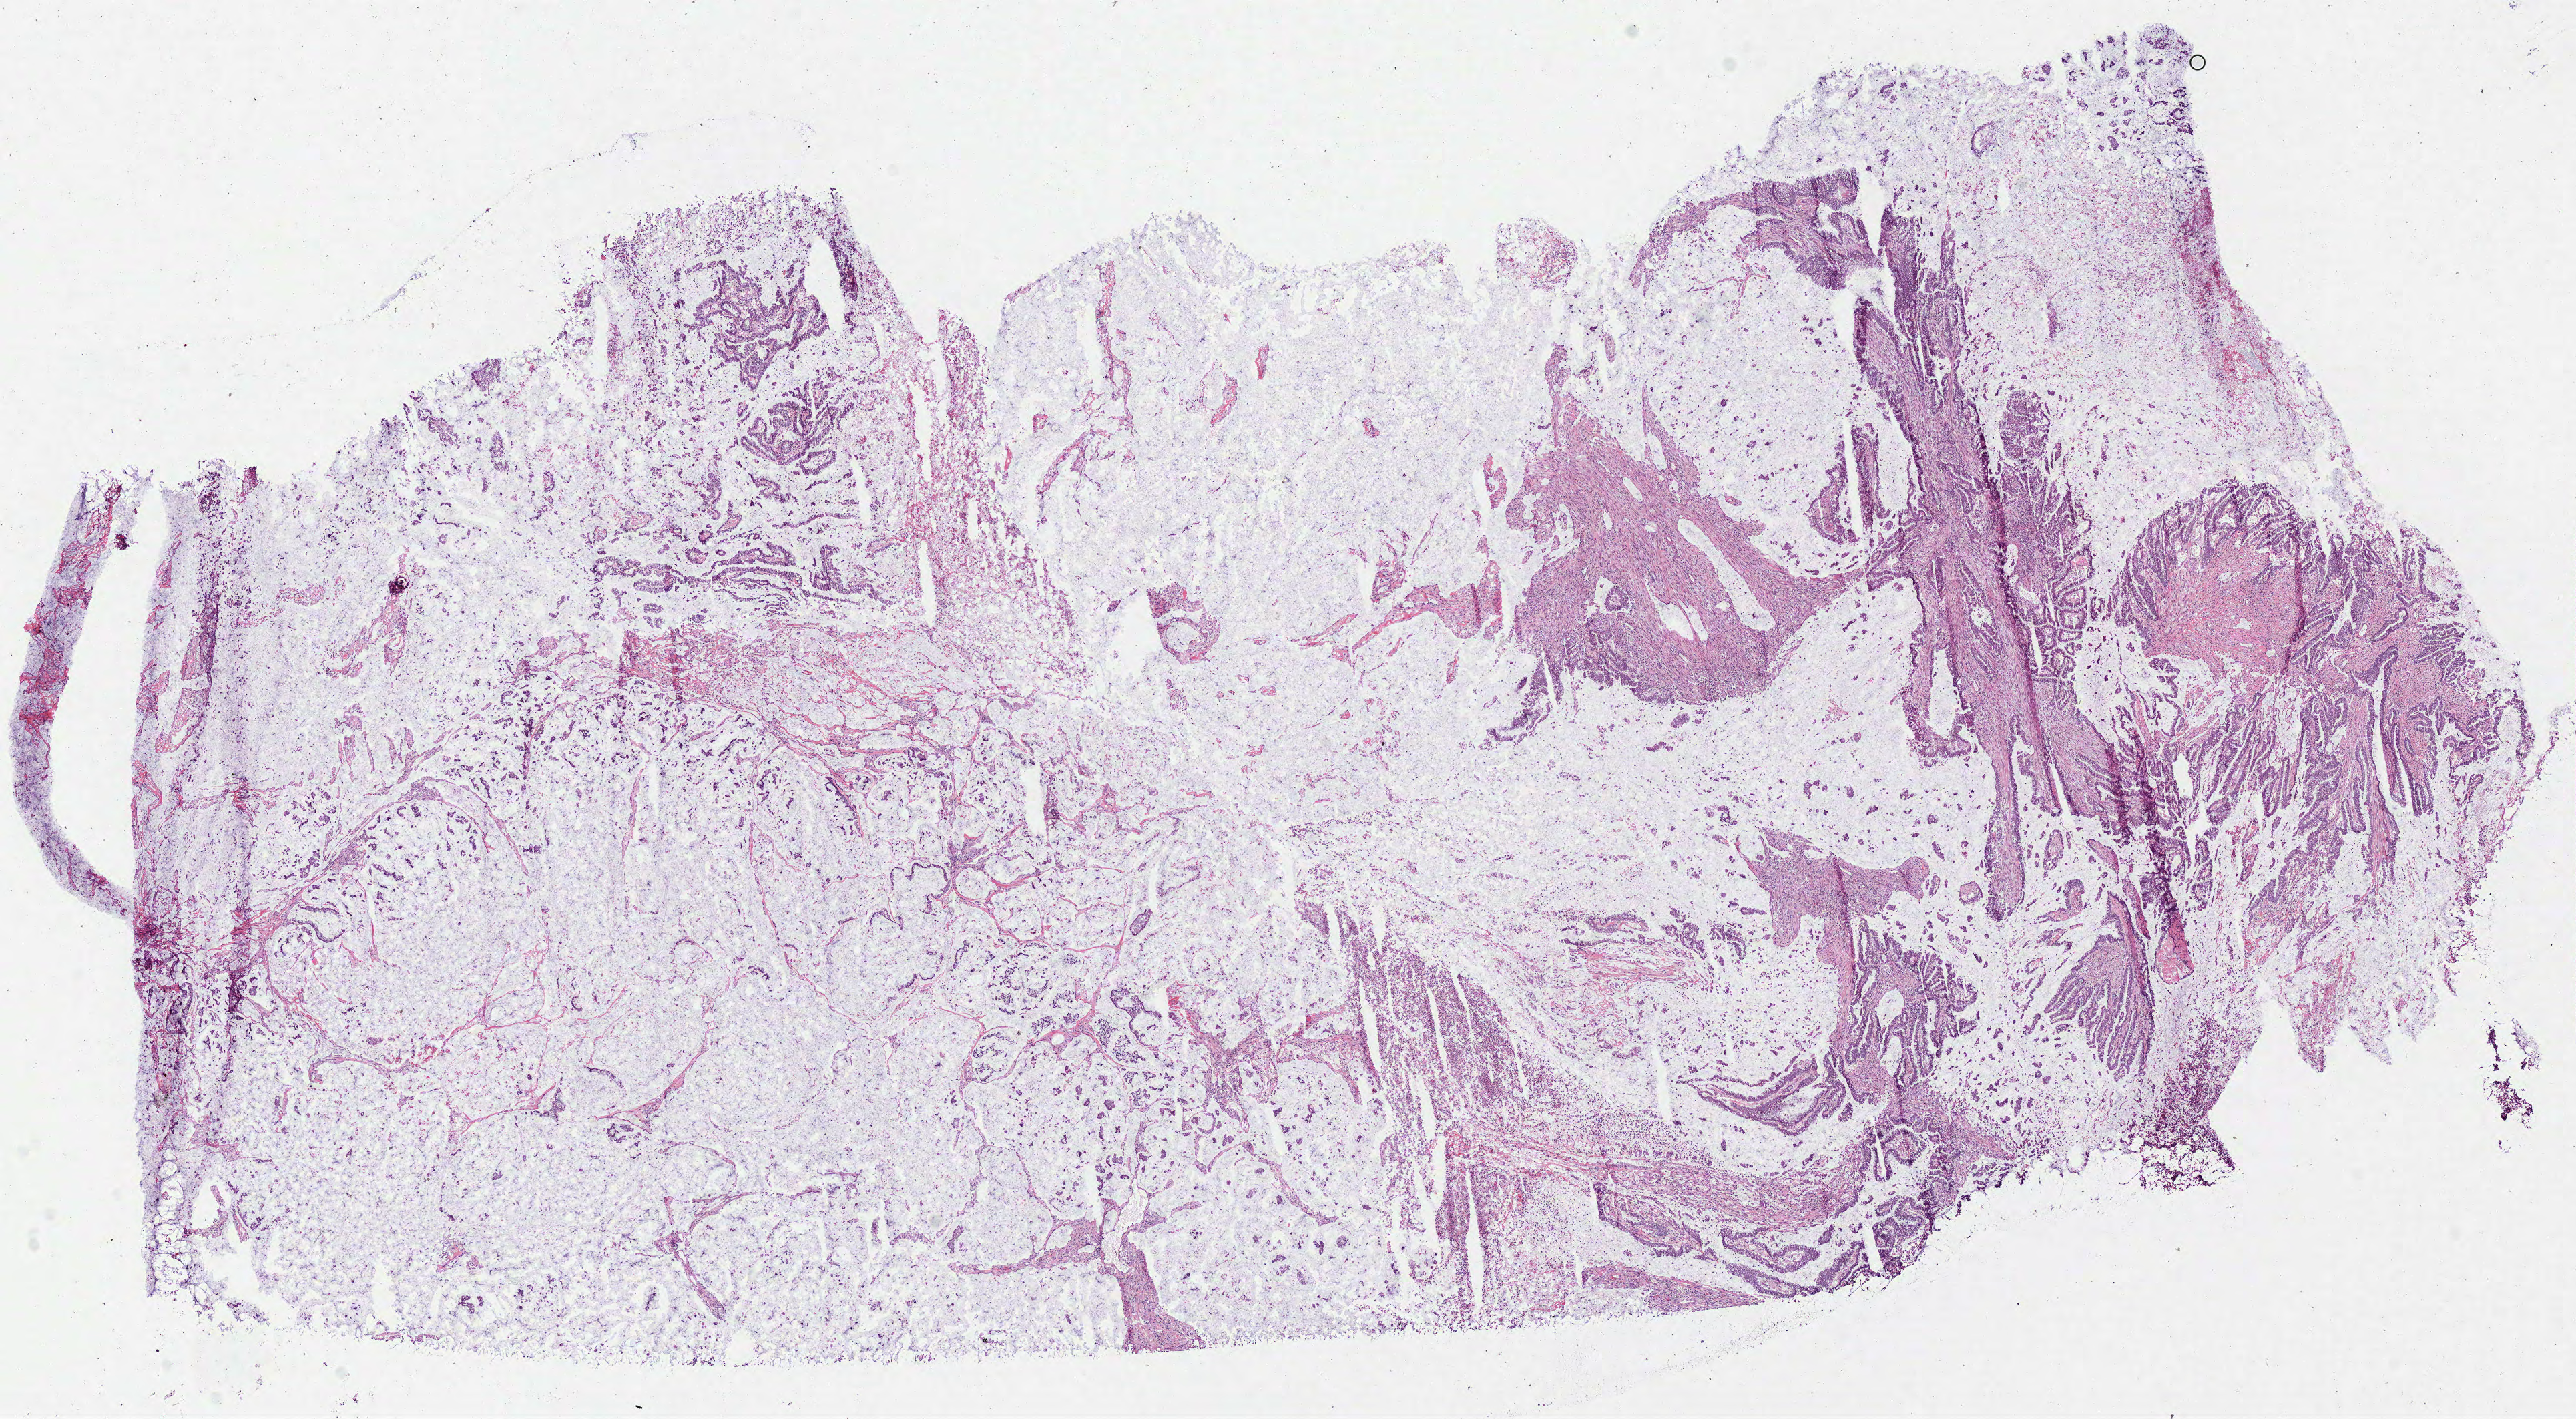
Hematoxylin and eosin (H&E) stained whole-slide image — shown as a low-resolution overview of the whole scanned area (about 15.2 x 8.4 mm); frozen section; colon, primary tumour sample. Patient: male, age at initial diagnosis 43 years. Pathologist review of this section (percent, as recorded): tumour nuclei 70%, necrosis 0%. Infiltration values recorded for this section: lymphocyte infiltration 5%, monocyte infiltration 5%, neutrophil infiltration 10%.
• diagnosis: Mucinous adenocarcinoma
• AJCC pathologic stage: IIIC (7th edition)